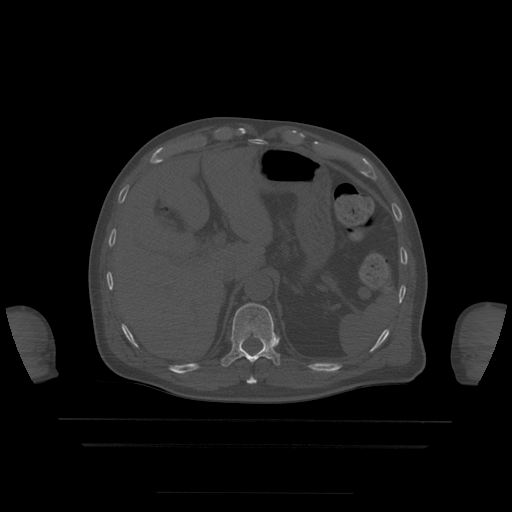
CT including the spine, one axial slice; slice 221 of 522 in the series (ordered by position); bone window (W 1800 / L 400 HU); 512 × 512 image matrix, field of view 436 × 436 mm. Patient age 68 years. From the clinical record (not read from this slice): primary cancer: urothelial.
Annotated regions visible in this slice (semi-automatic segmentation, software-assisted and operator-edited):
- T10 vertebra: box from (x=247, y=377) to (x=257, y=384) px
- T11 vertebra: (x=221, y=303)–(x=280, y=367)